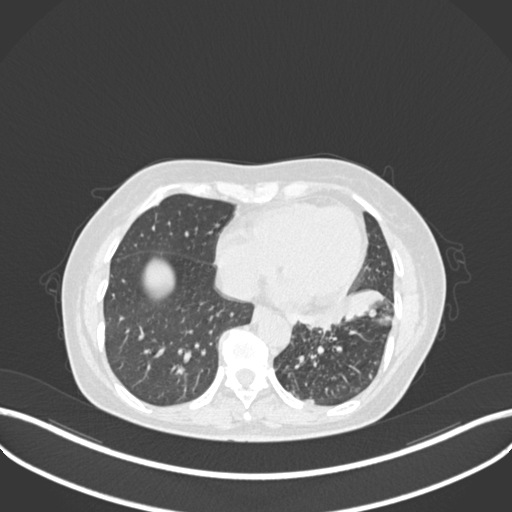
Chest CT, one axial slice. Slice 87 of 270 in the series (ordered by position). Reconstruction kernel B30f. 120 kVp. Lung window (W 1500 / L -600 HU). 512 × 512 image matrix, field of view 400 × 400 mm. Female patient, age 63 years. Case-level facts recorded for this patient, not image findings: clinical TNM (as recorded): T1b N0 M0.
Structures marked on this image (rectangle marked by the reading radiologist):
- lung tumour (recorded histology: adenocarcinoma): box from (x=299, y=288) to (x=394, y=330) px